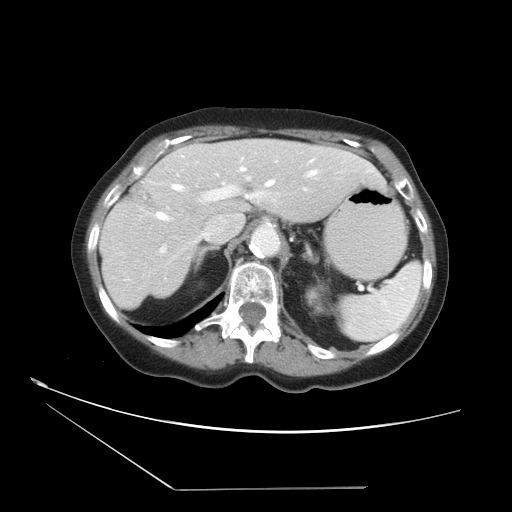
Contrast-enhanced abdominal CT, one axial slice. Slice 24 of 36 in the series (ordered by position). 120 kVp. Intravenous contrast given. Soft-tissue window (W 400 / L 40 HU). 5 mm slice thickness. 512 × 512 image matrix, field of view 384 × 384 mm. Female patient, age 81 years. From the clinical record (not read from this slice): diagnosis: colorectal cancer liver metastases, imaged before liver resection; multiple liver metastases: no.
Structures marked on this image (outlined manually by an expert reader):
- hepatic veins: bounding box <157,158,320,222> (left, top, right, bottom; pixels)
- liver: <99,140,386,310>
- planned liver remnant (the part of the liver to remain after resection): <99,140,386,310>
- portal vein (with intrahepatic branches): <161,177,259,252>